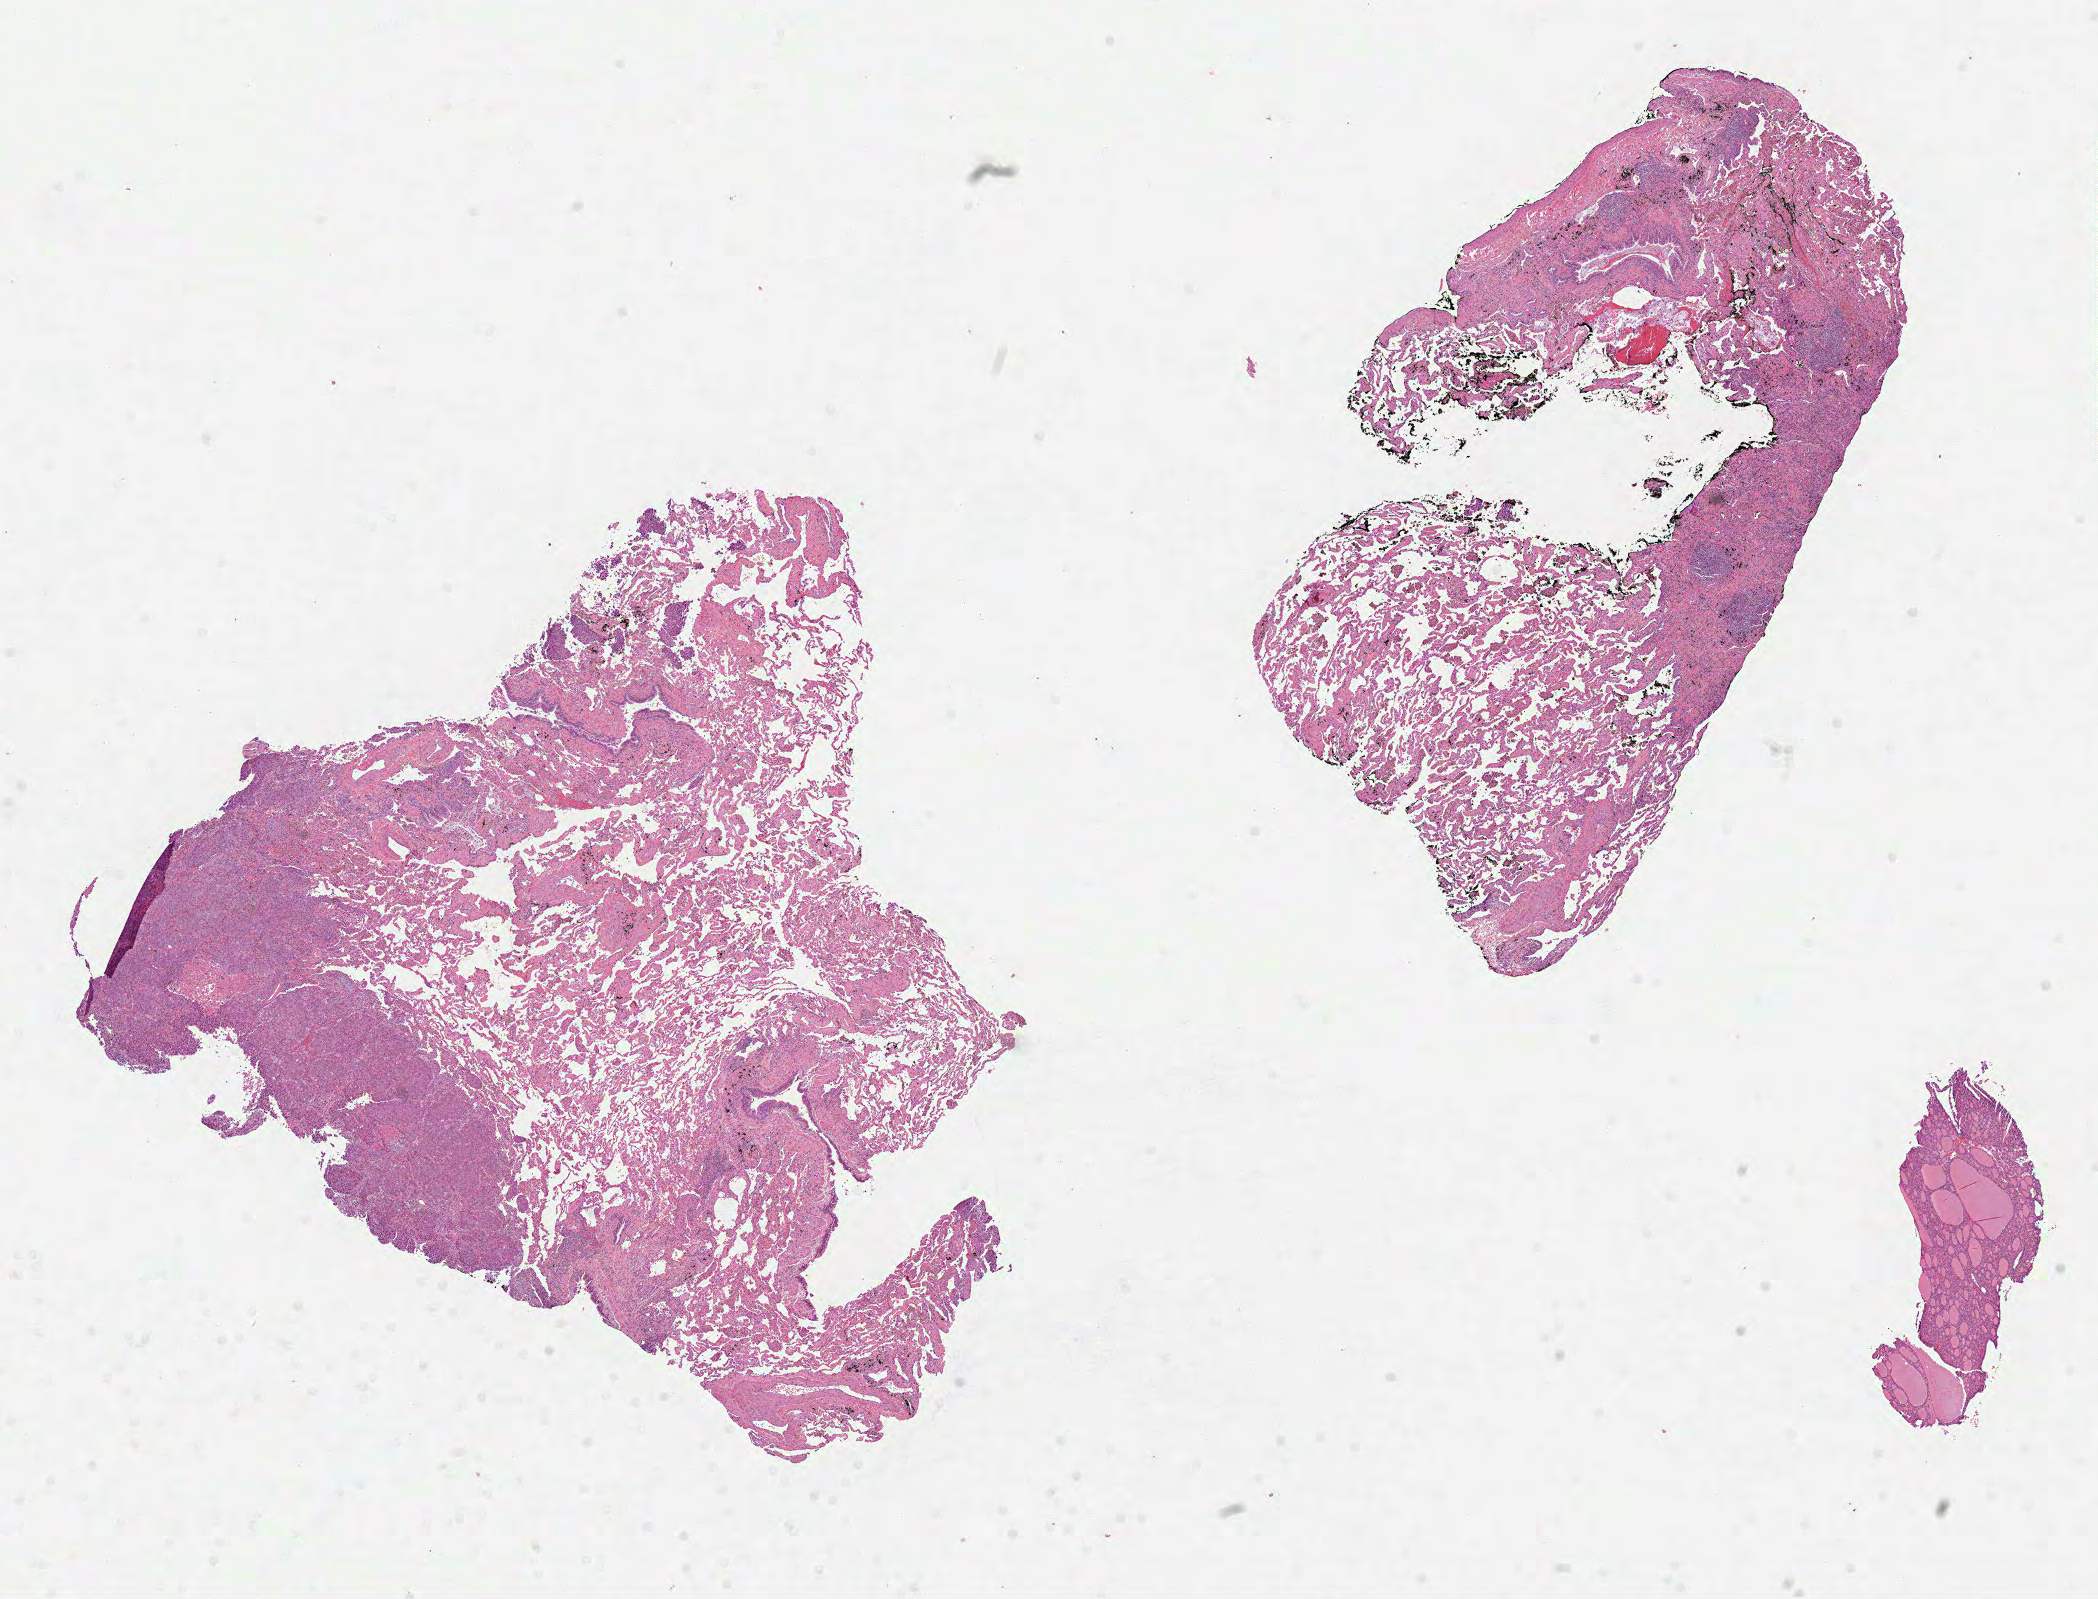
Digitized Hematoxylin and eosin (H&E) stained tissue section (whole slide) — a low-resolution overview of the entire scanned area, about 16.9 x 12.9 mm, formalin-fixed paraffin-embedded (FFPE) diagnostic section, lung, primary tumour sample. Patient: male, age at initial diagnosis 60 years.
Histologic diagnosis: Adenocarcinoma, NOS (upper lobe, lung). Laterality: right. AJCC pathologic stage: IA (7th edition).